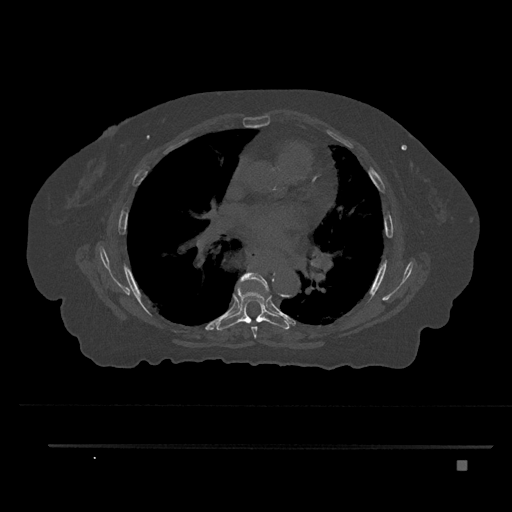
CT including the spine, one axial slice. Slice 500 of 797 in the series (ordered by position). 120 kVp. Bone window (W 1800 / L 400 HU). 0.5 mm slice thickness. 512 × 512 image matrix. Female patient, age 76 years. From the clinical record (not read from this slice): primary cancer: lung; vertebrae with lytic lesions (as recorded): T11, L3.
Annotated regions visible in this slice (semi-automatic segmentation, software-assisted and operator-edited):
- T6 vertebra: box from (x=238, y=272) to (x=269, y=338) px
- T7 vertebra: (x=216, y=285)–(x=290, y=331)